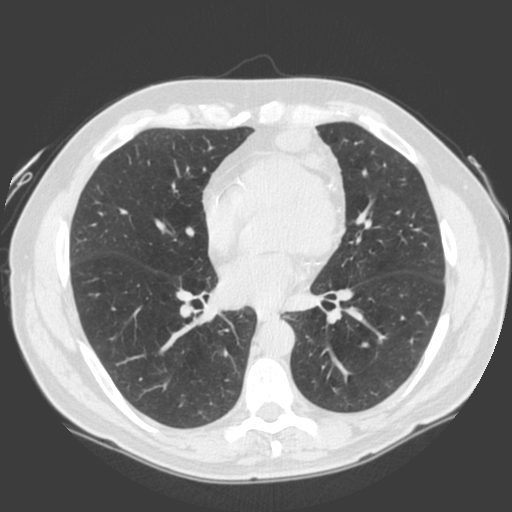
Low-dose screening chest CT, one axial slice. 120 kVp. Lung window (W 1500 / L -600 HU). 2 mm slice thickness. 512 × 512 image matrix, field of view 360 × 360 mm.
Structures marked on this image (manually delineated by an expert):
- lesion 1 (tumor, lower lobe of left lung): bounding box [x1, y1, x2, y2] px = [274, 125, 341, 176]